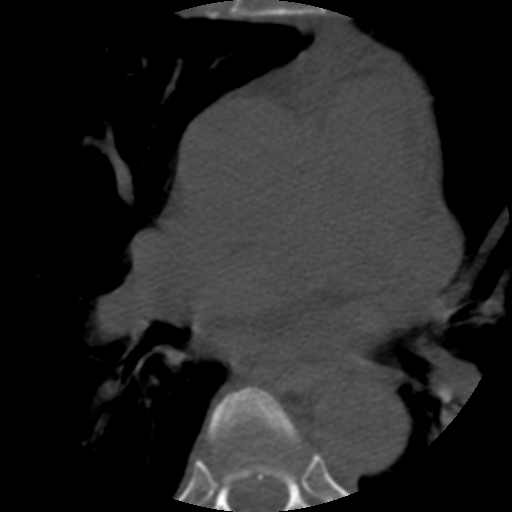
CT including the spine, one axial slice; slice 364 of 508 in the series (ordered by position); bone window (W 1800 / L 400 HU); 1.25 mm slice thickness; 512 × 512 image matrix, field of view 160 × 160 mm. Patient age 57 years. From the clinical record (not read from this slice): primary cancer: prostate.
Annotated regions visible in this slice (semi-automatic segmentation, software-assisted and operator-edited):
- T5 vertebra: bounding box [x1, y1, x2, y2] px = [209, 387, 303, 463]
- T6 vertebra: [212, 454, 310, 512]